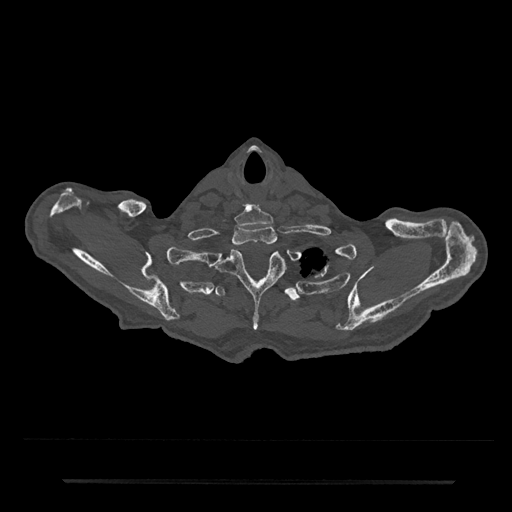
CT including the spine, one axial slice. Slice 700 of 797 in the series (ordered by position). 120 kVp. Bone window (W 1800 / L 400 HU). 0.5 mm slice thickness. 512 × 512 image matrix, field of view 427 × 427 mm. Male patient, age 74 years. From the clinical record (not read from this slice): primary cancer: prostate.
Outlined on this slice (semi-automatically segmented with operator editing):
- T1 vertebra: bounding box [x1, y1, x2, y2] px = [233, 225, 277, 245]
- T2 vertebra: [213, 250, 283, 331]
- T3 vertebra: [215, 286, 300, 302]